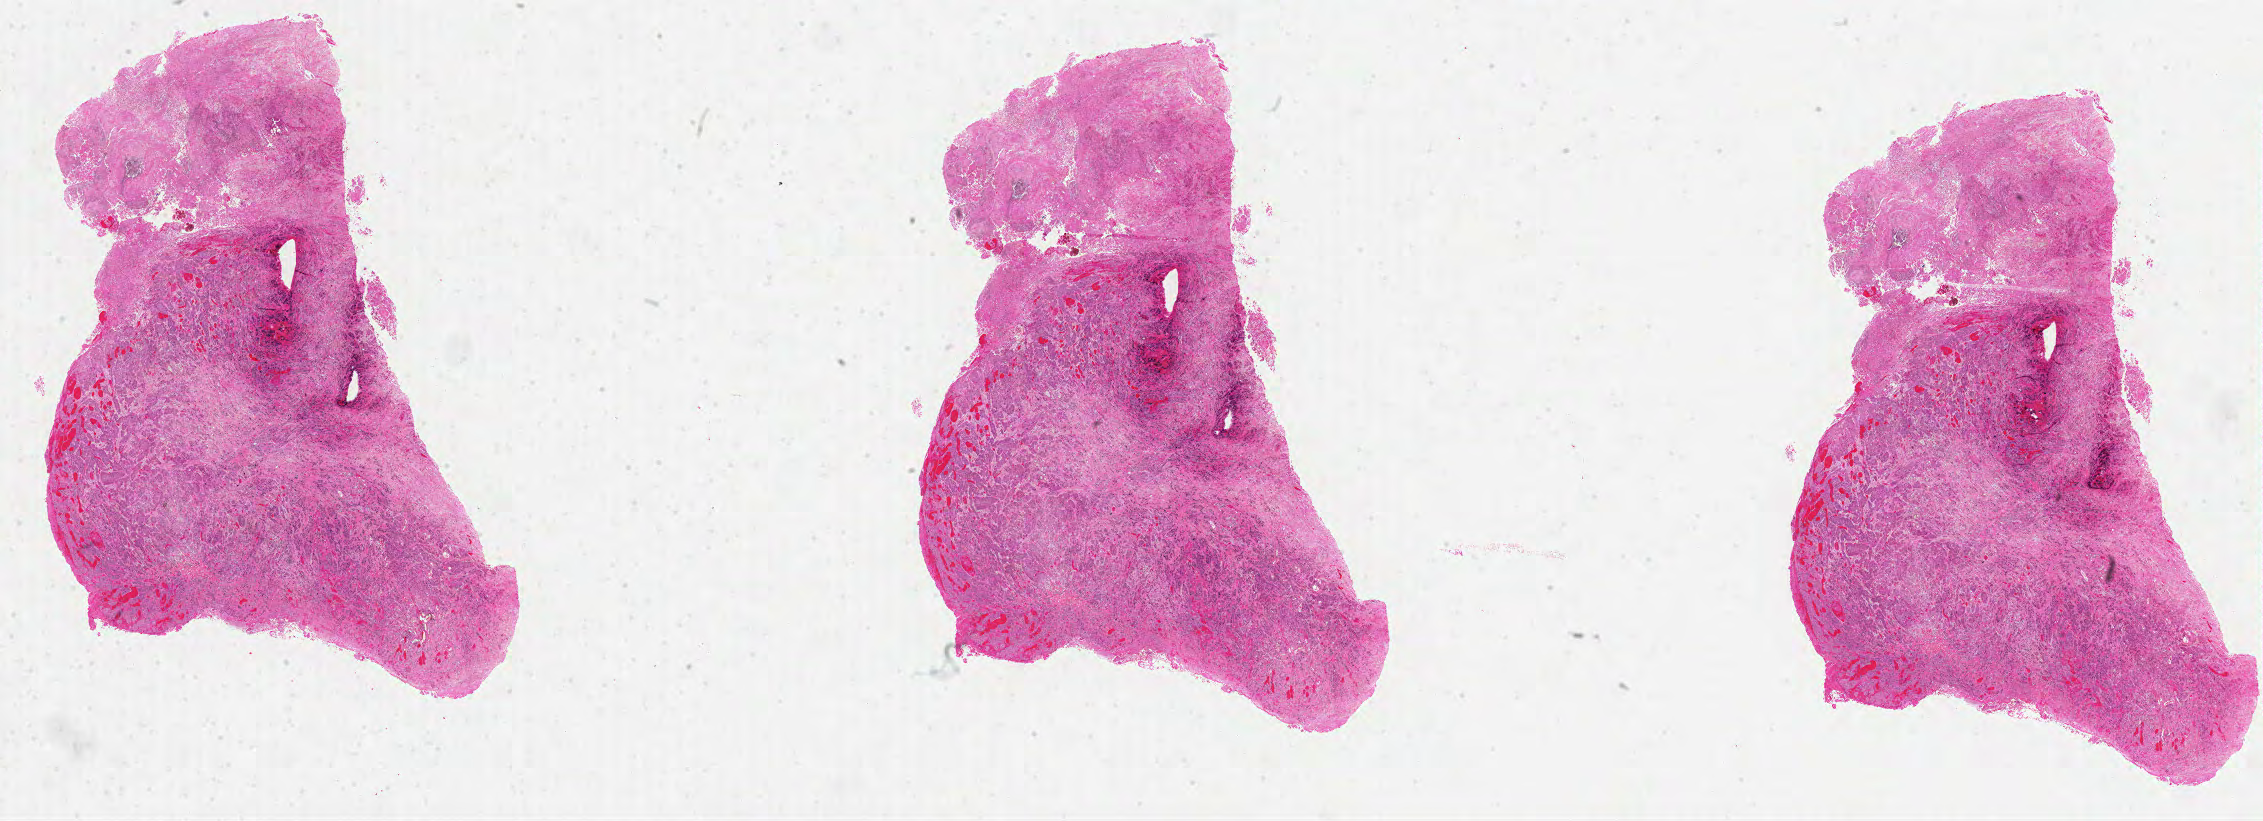
H&E-stained whole-slide image, low-resolution overview of the scanned area, about 36.5 x 13.2 mm; formalin-fixed paraffin-embedded (FFPE) diagnostic section; head and neck, primary tumour sample. Male, age 49 years at initial diagnosis. Histologic grade: G2 (moderately differentiated).
• histologic diagnosis: Squamous cell carcinoma, NOS
• AJCC pathologic stage: III (6th edition)
• lymph nodes positive (case pathology): 0 of 48 examined